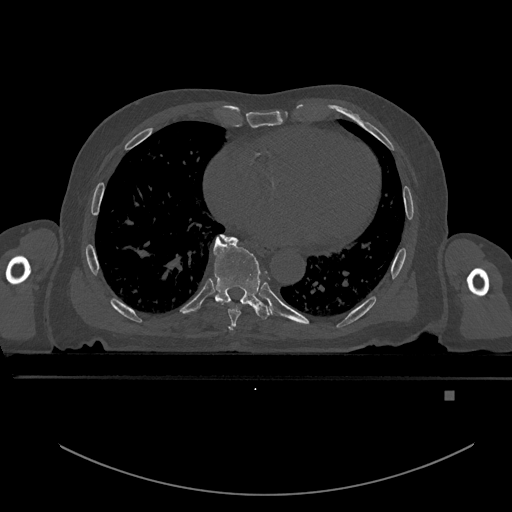
CT including the spine, one axial slice. Position 222 of 969 along the scan axis. Bone window (W 1800 / L 400 HU). 512 × 512 image matrix. Patient: male, 82 years. From the clinical record (not read from this slice): primary cancer: prostate; vertebrae with lytic lesions (as recorded): T11, T9, T8, T2.
Annotated regions visible in this slice (semi-automatically segmented with operator editing):
- T6 vertebra: bounding box <229,327,232,332> (left, top, right, bottom; pixels)
- T7 vertebra: <221,235,241,326>
- T8 vertebra: <213,236,271,319>